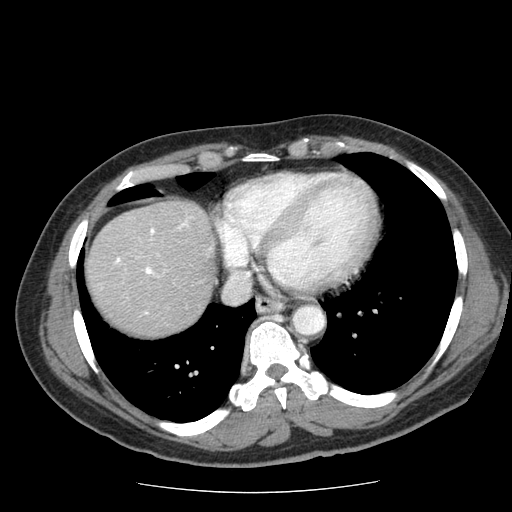
Contrast-enhanced abdominal CT (liver protocol), one axial slice; position 66 of 85 along the scan axis; soft-tissue window (W 400 / L 40 HU); 512 × 512 image matrix. From the clinical record (not read from this slice): diagnosis: hepatocellular carcinoma (patient treated with transarterial chemoembolisation; whether this scan precedes or follows treatment is not stated here); TNM stage (as recorded): Stage-IIIA; Child-Pugh class: A; tumour nodularity: multinodular; tumour size: 8 cm.
Annotated regions visible in this slice (semi-automatically segmented with operator editing):
- liver parenchyma outside the tumour (the mass and vessels are separate outlines, so this box may not span the whole liver): bounding box (x1, y1, x2, y2) in pixels: (86, 200, 216, 336)
- liver vessels: (115, 221, 187, 275)